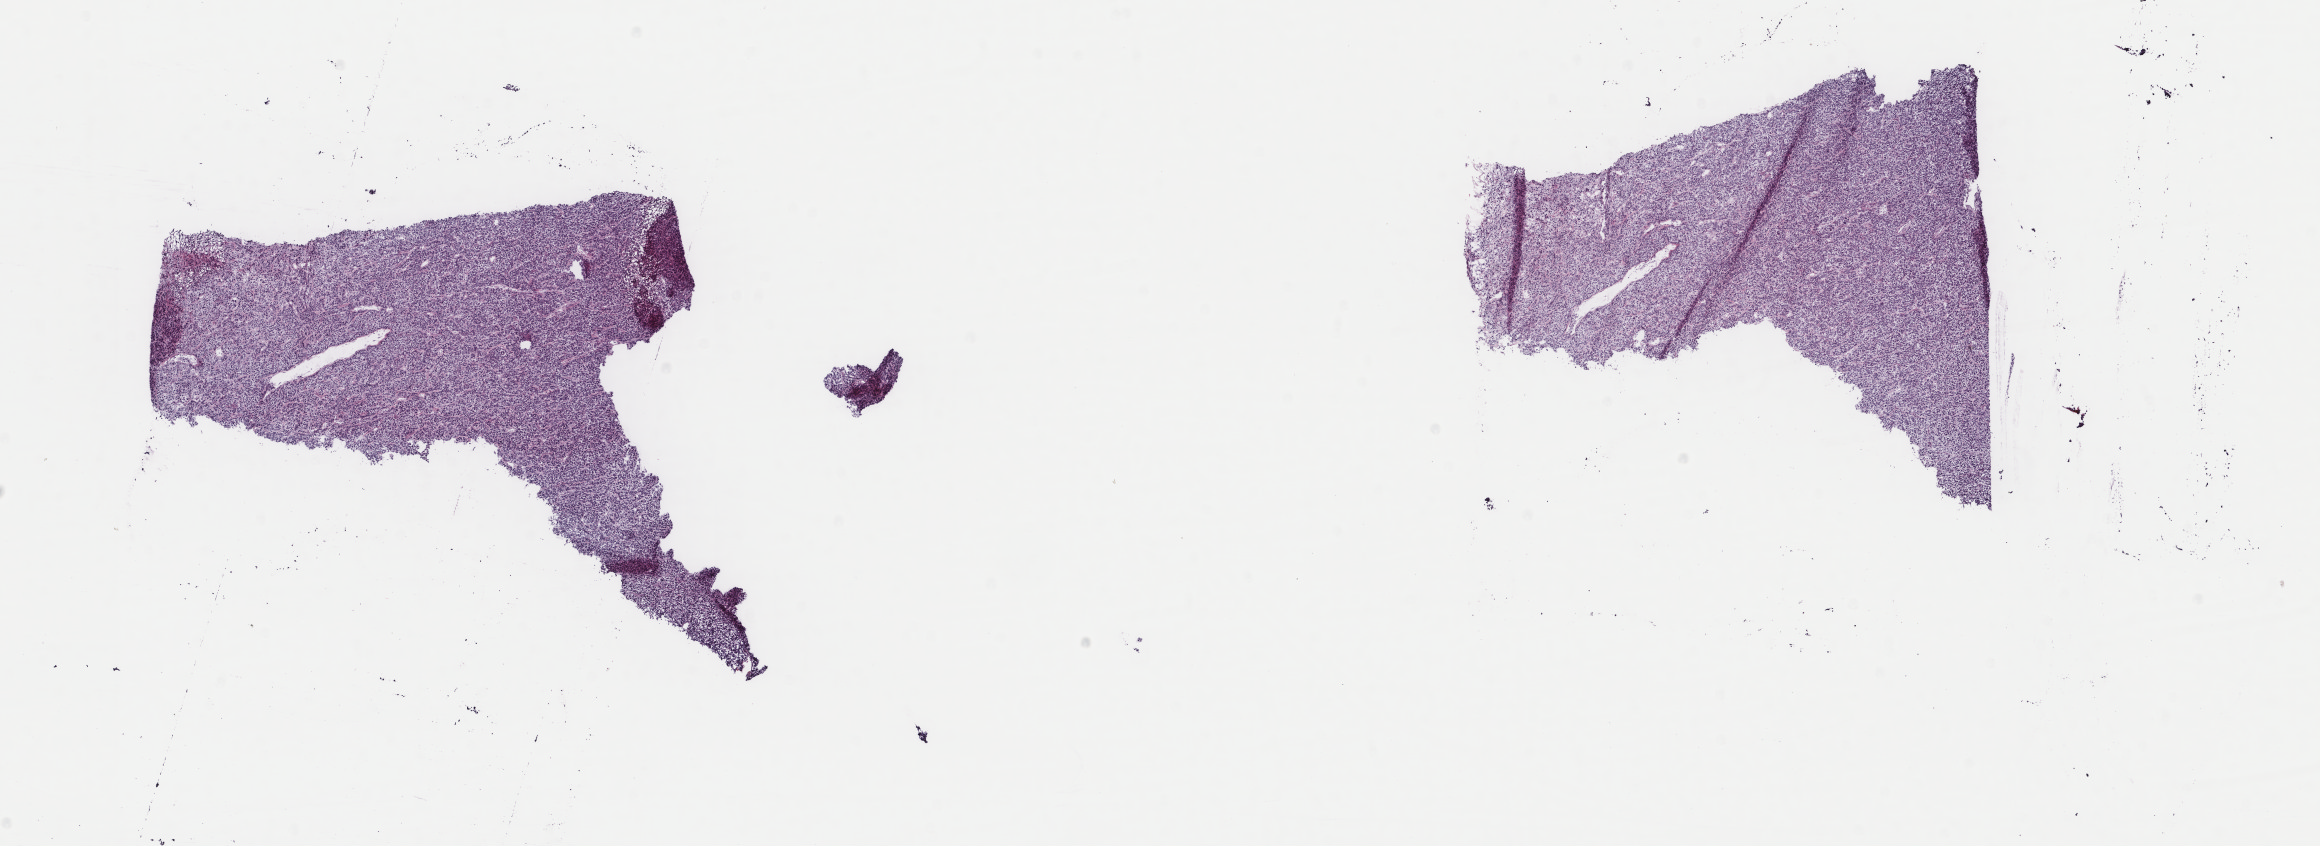
Digitized H&E tissue section (whole slide), a low-resolution overview of the entire scanned area, about 18.4 x 6.7 mm; frozen section from the top of the tissue portion; primary tumour sample from the corpus uteri. Female patient; age at initial diagnosis 55 years. Slide review estimates, as recorded: tumour cells 100%, tumour nuclei 85%, normal cells 0%, stromal cells 0%, necrosis 0%. Inflammatory infiltration, as recorded: lymphocyte infiltration 1%, monocyte infiltration 0%, neutrophil infiltration 0%.
Histologic diagnosis: Leiomyosarcoma, NOS (myometrium).